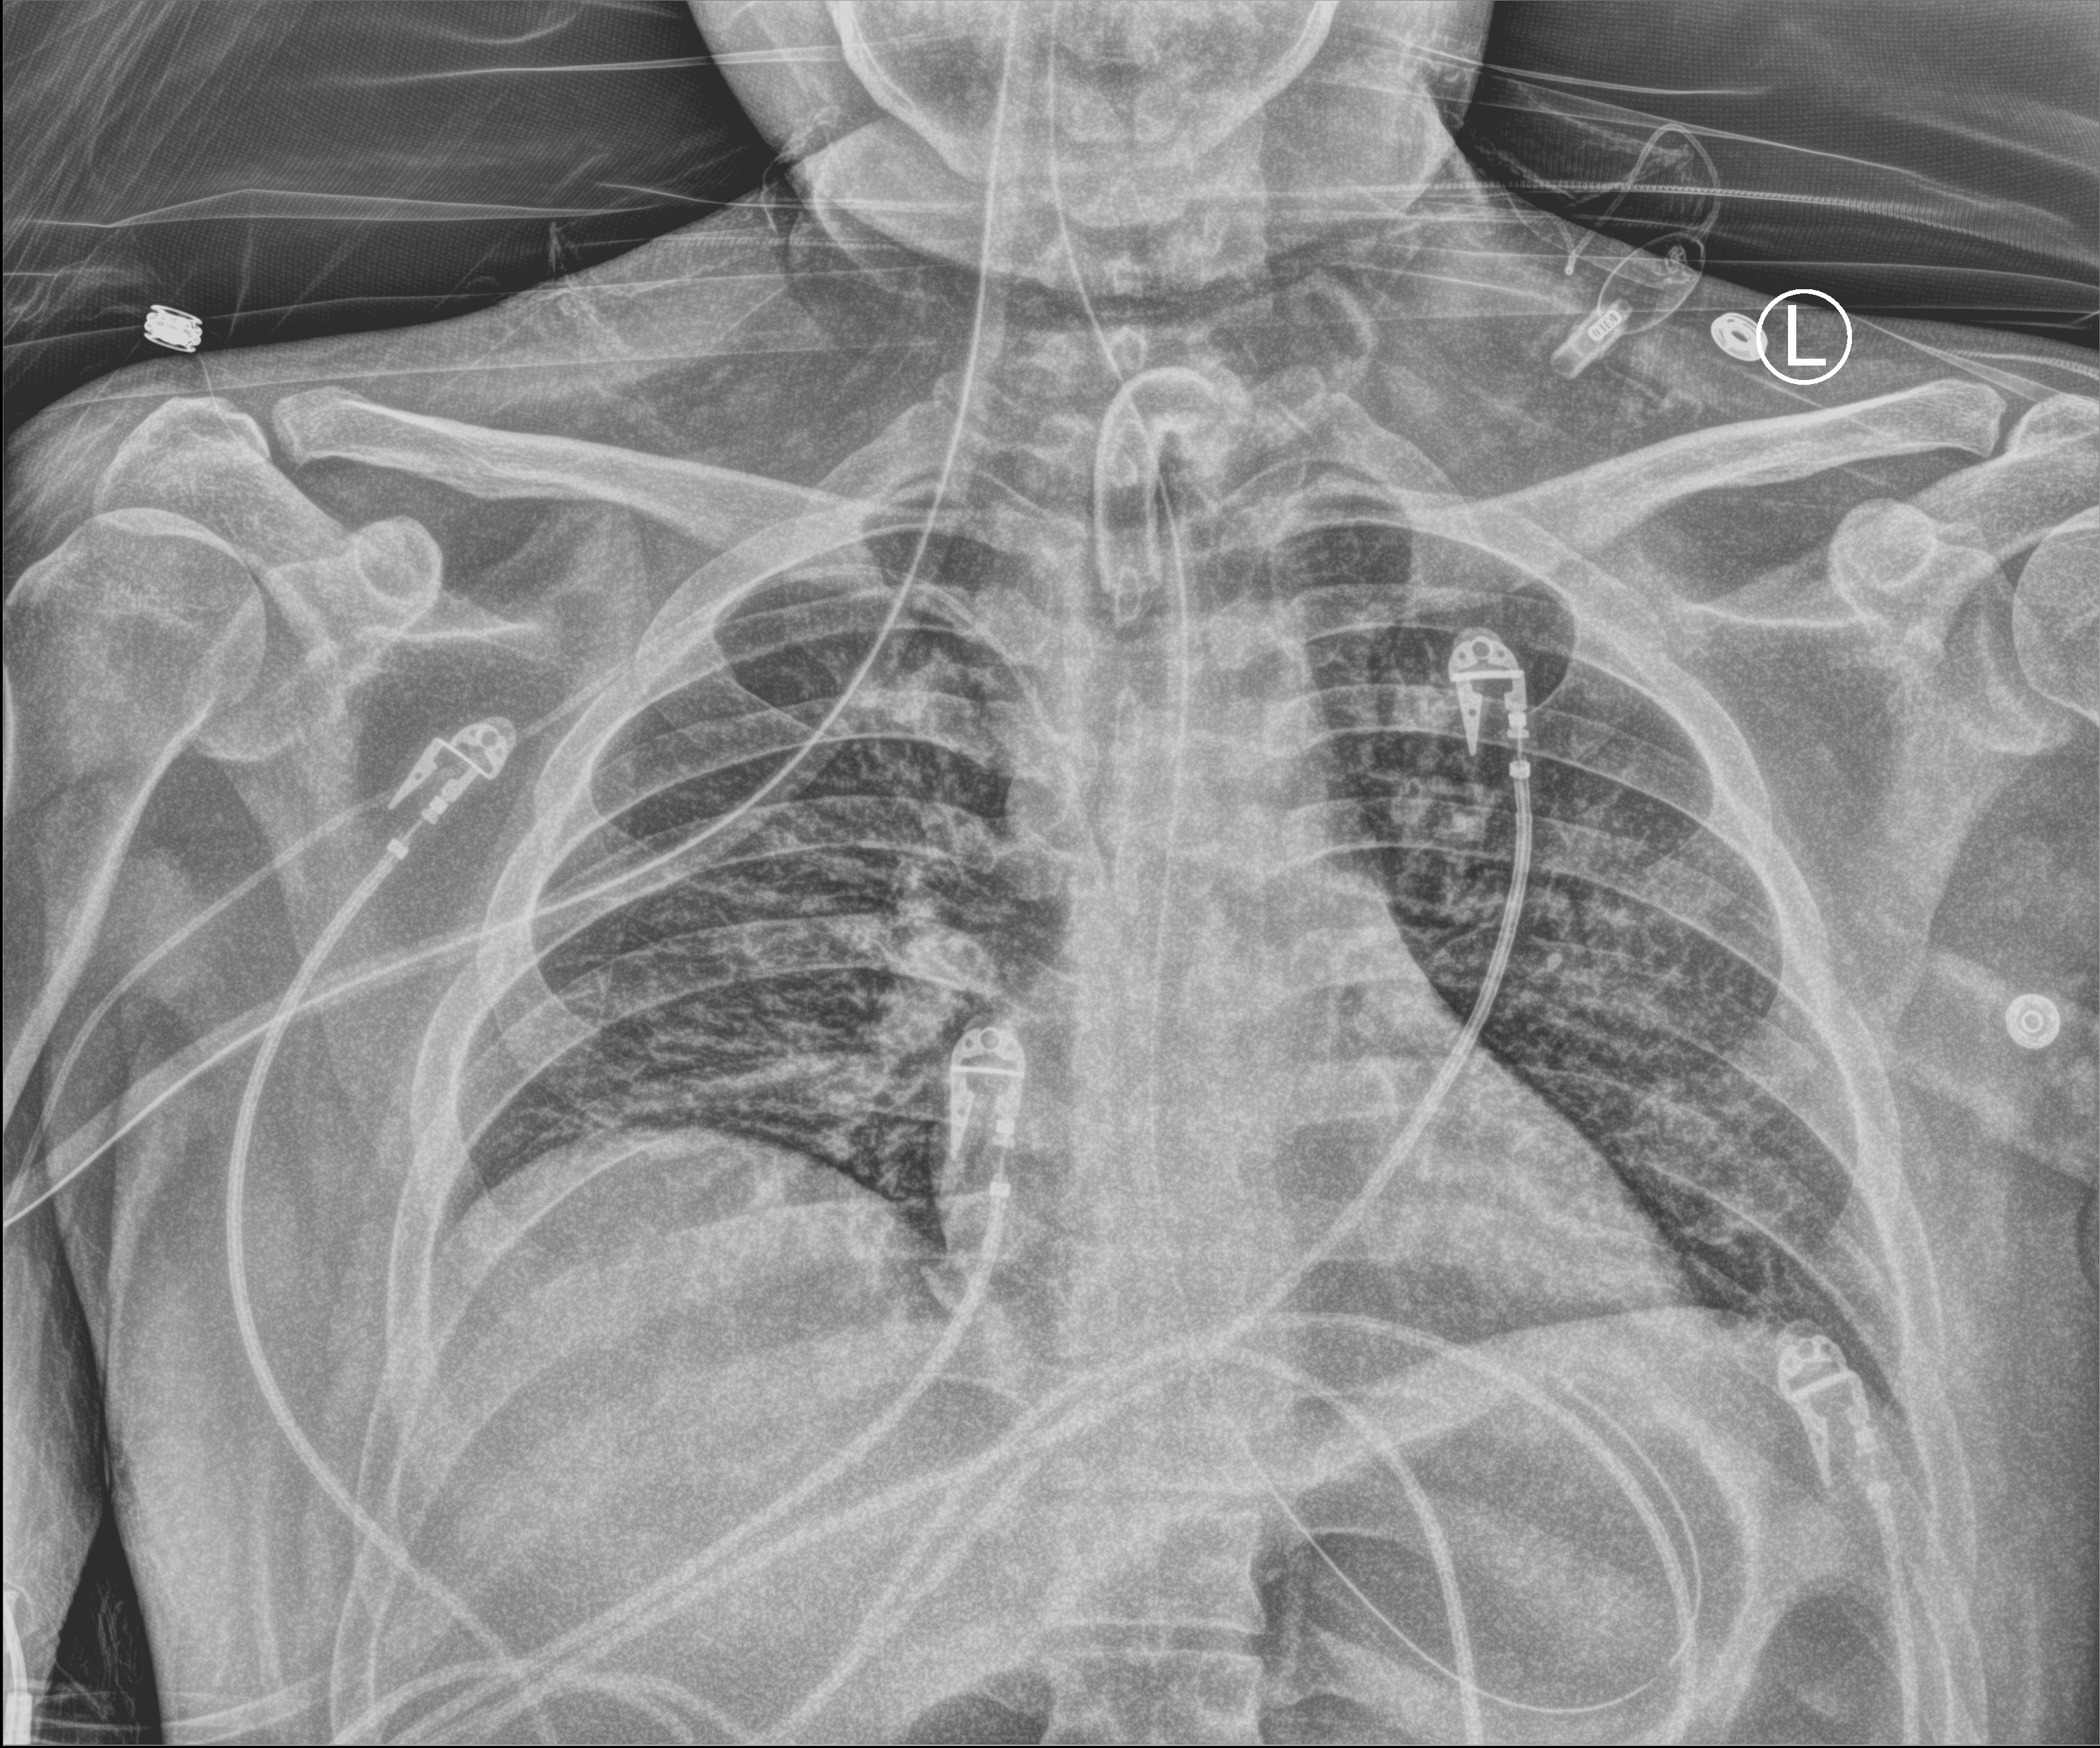
Chest X-ray (portable); anteroposterior (AP) projection. Patient hospitalised with COVID-19; male, aged 18–59 years.
From the hospital-stay record, not from the radiograph (when in the stay this image was taken is not recorded): length of hospital stay: 44 days.